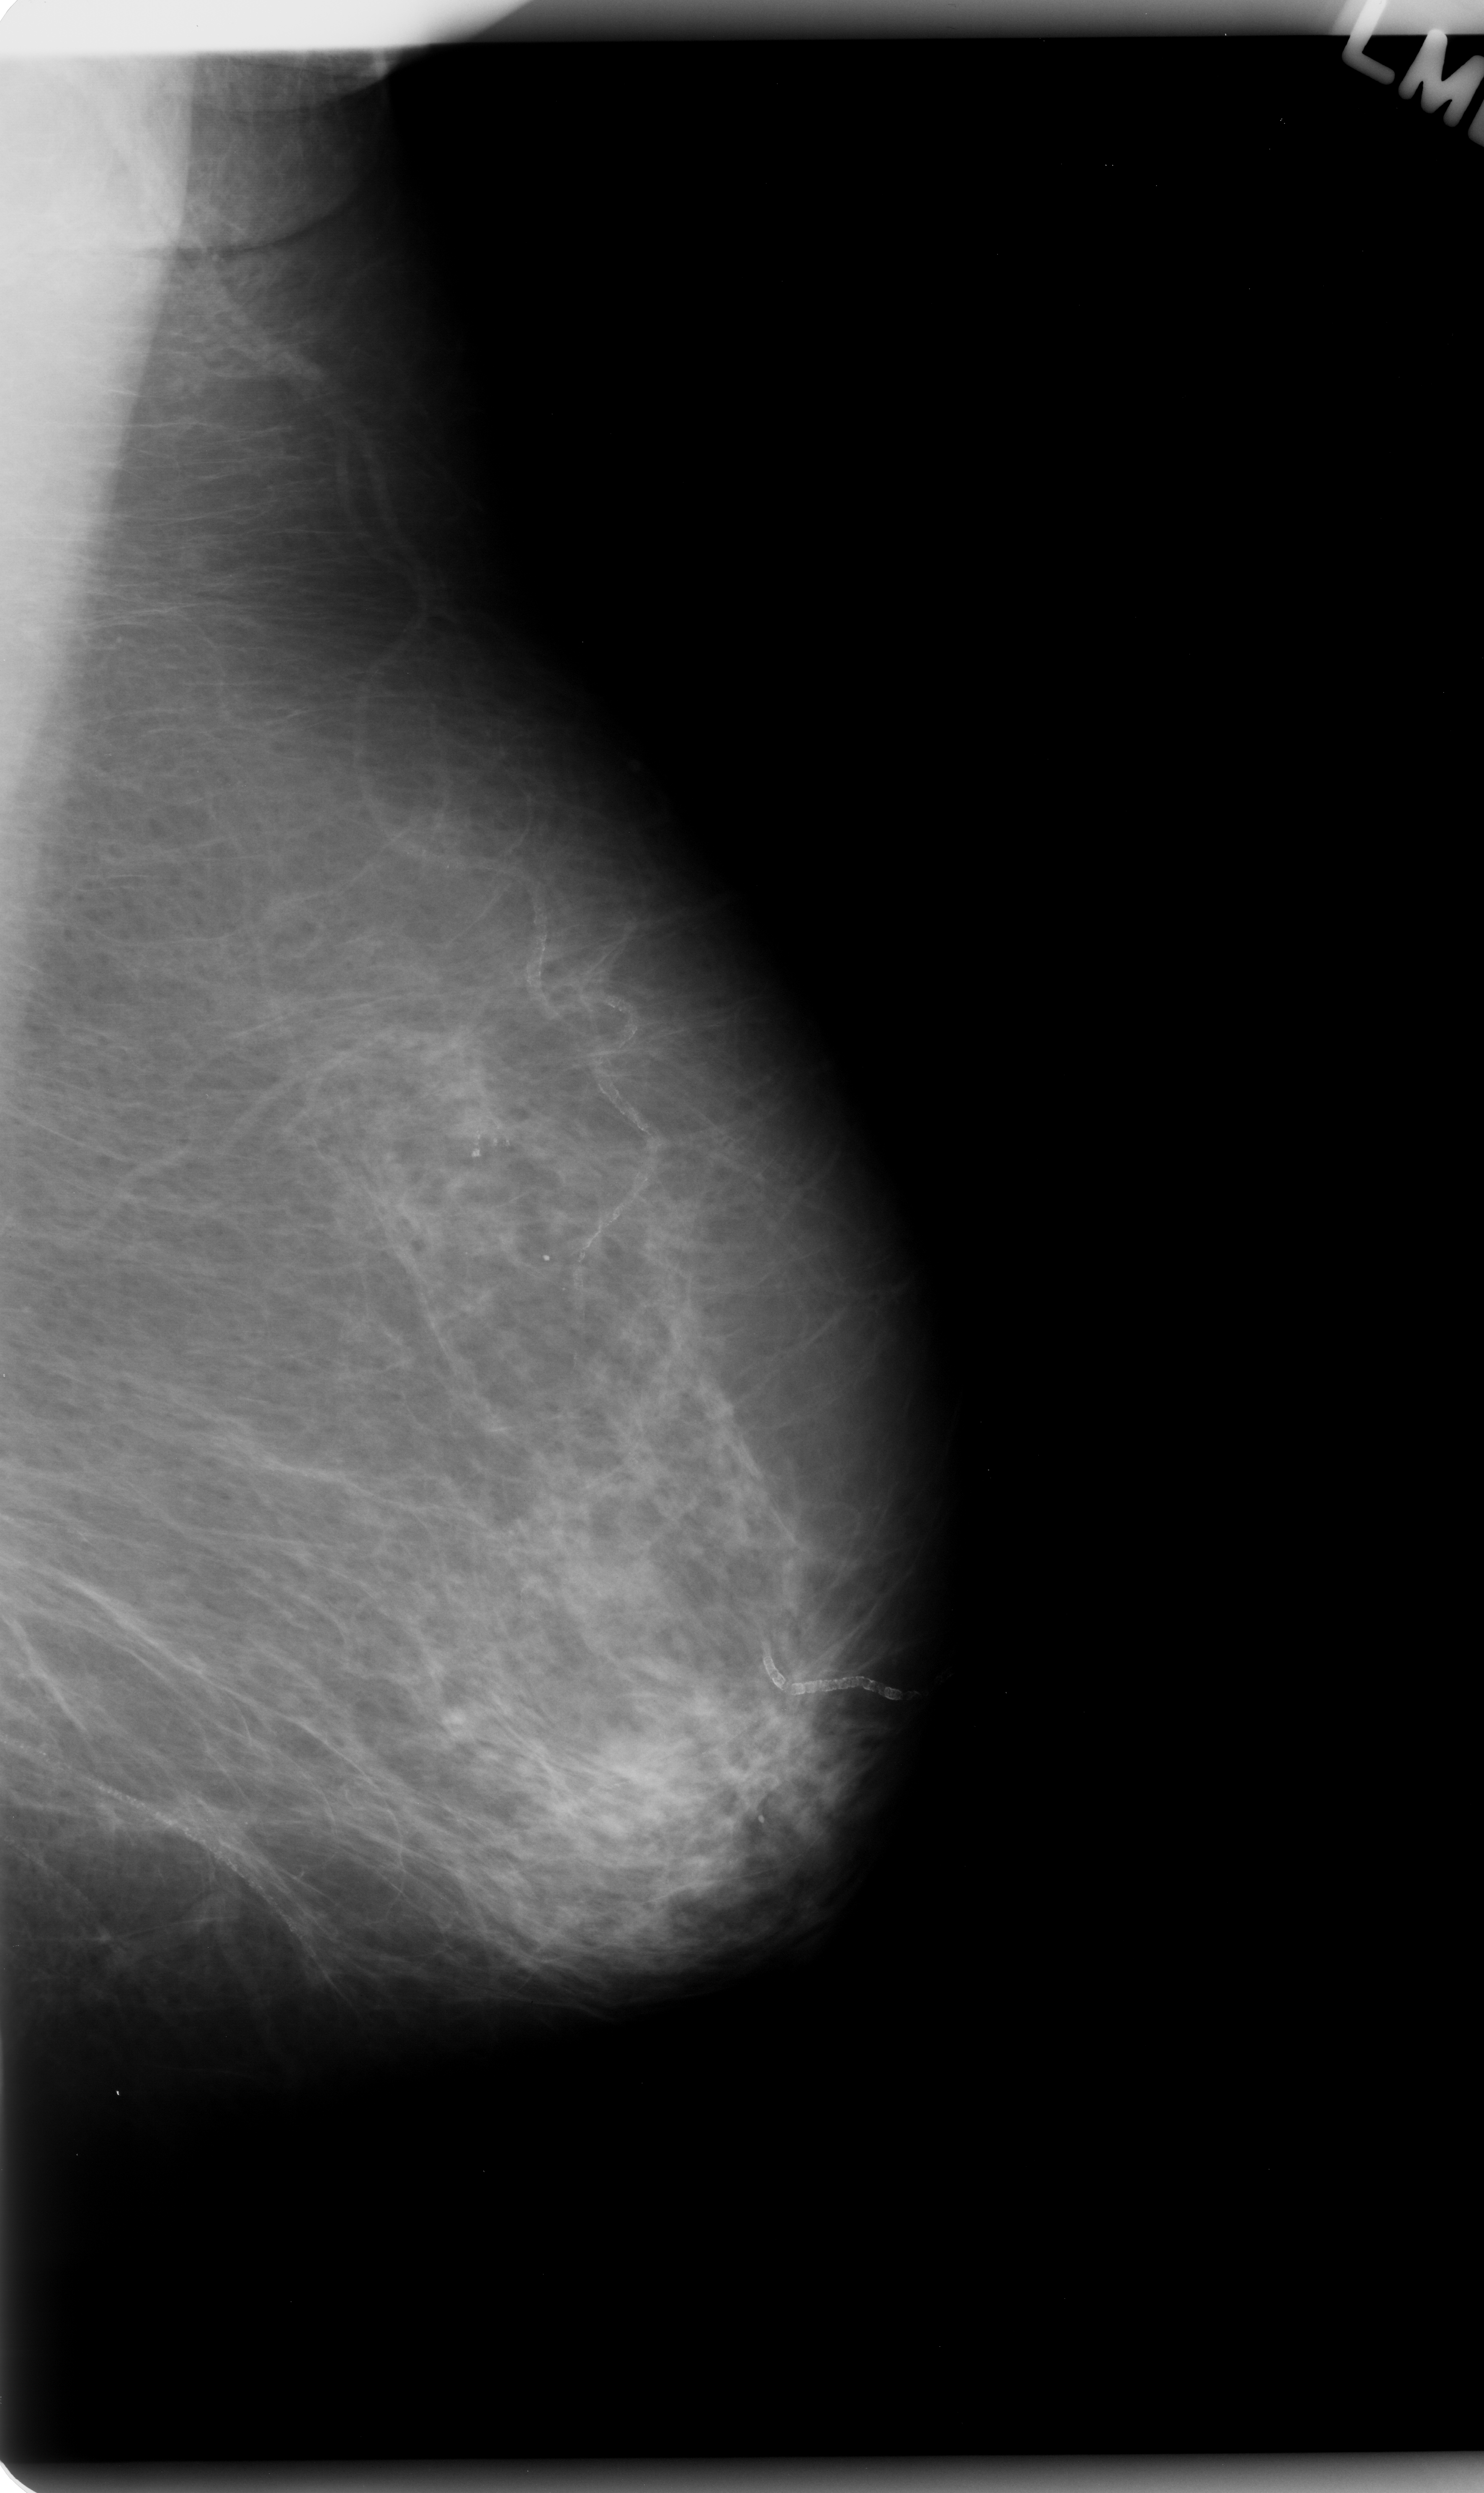
Mammogram (digitized film); left breast; MLO view.
Marked findings (only marked abnormalities are described; nothing is implied about the rest of the image): calcifications, morphology pleomorphic, distribution clustered; BI-RADS assessment category 4; subtlety rating 5 on a 1 (subtle) to 5 (obvious) scale; pathology result (as recorded, not read from the image): benign.